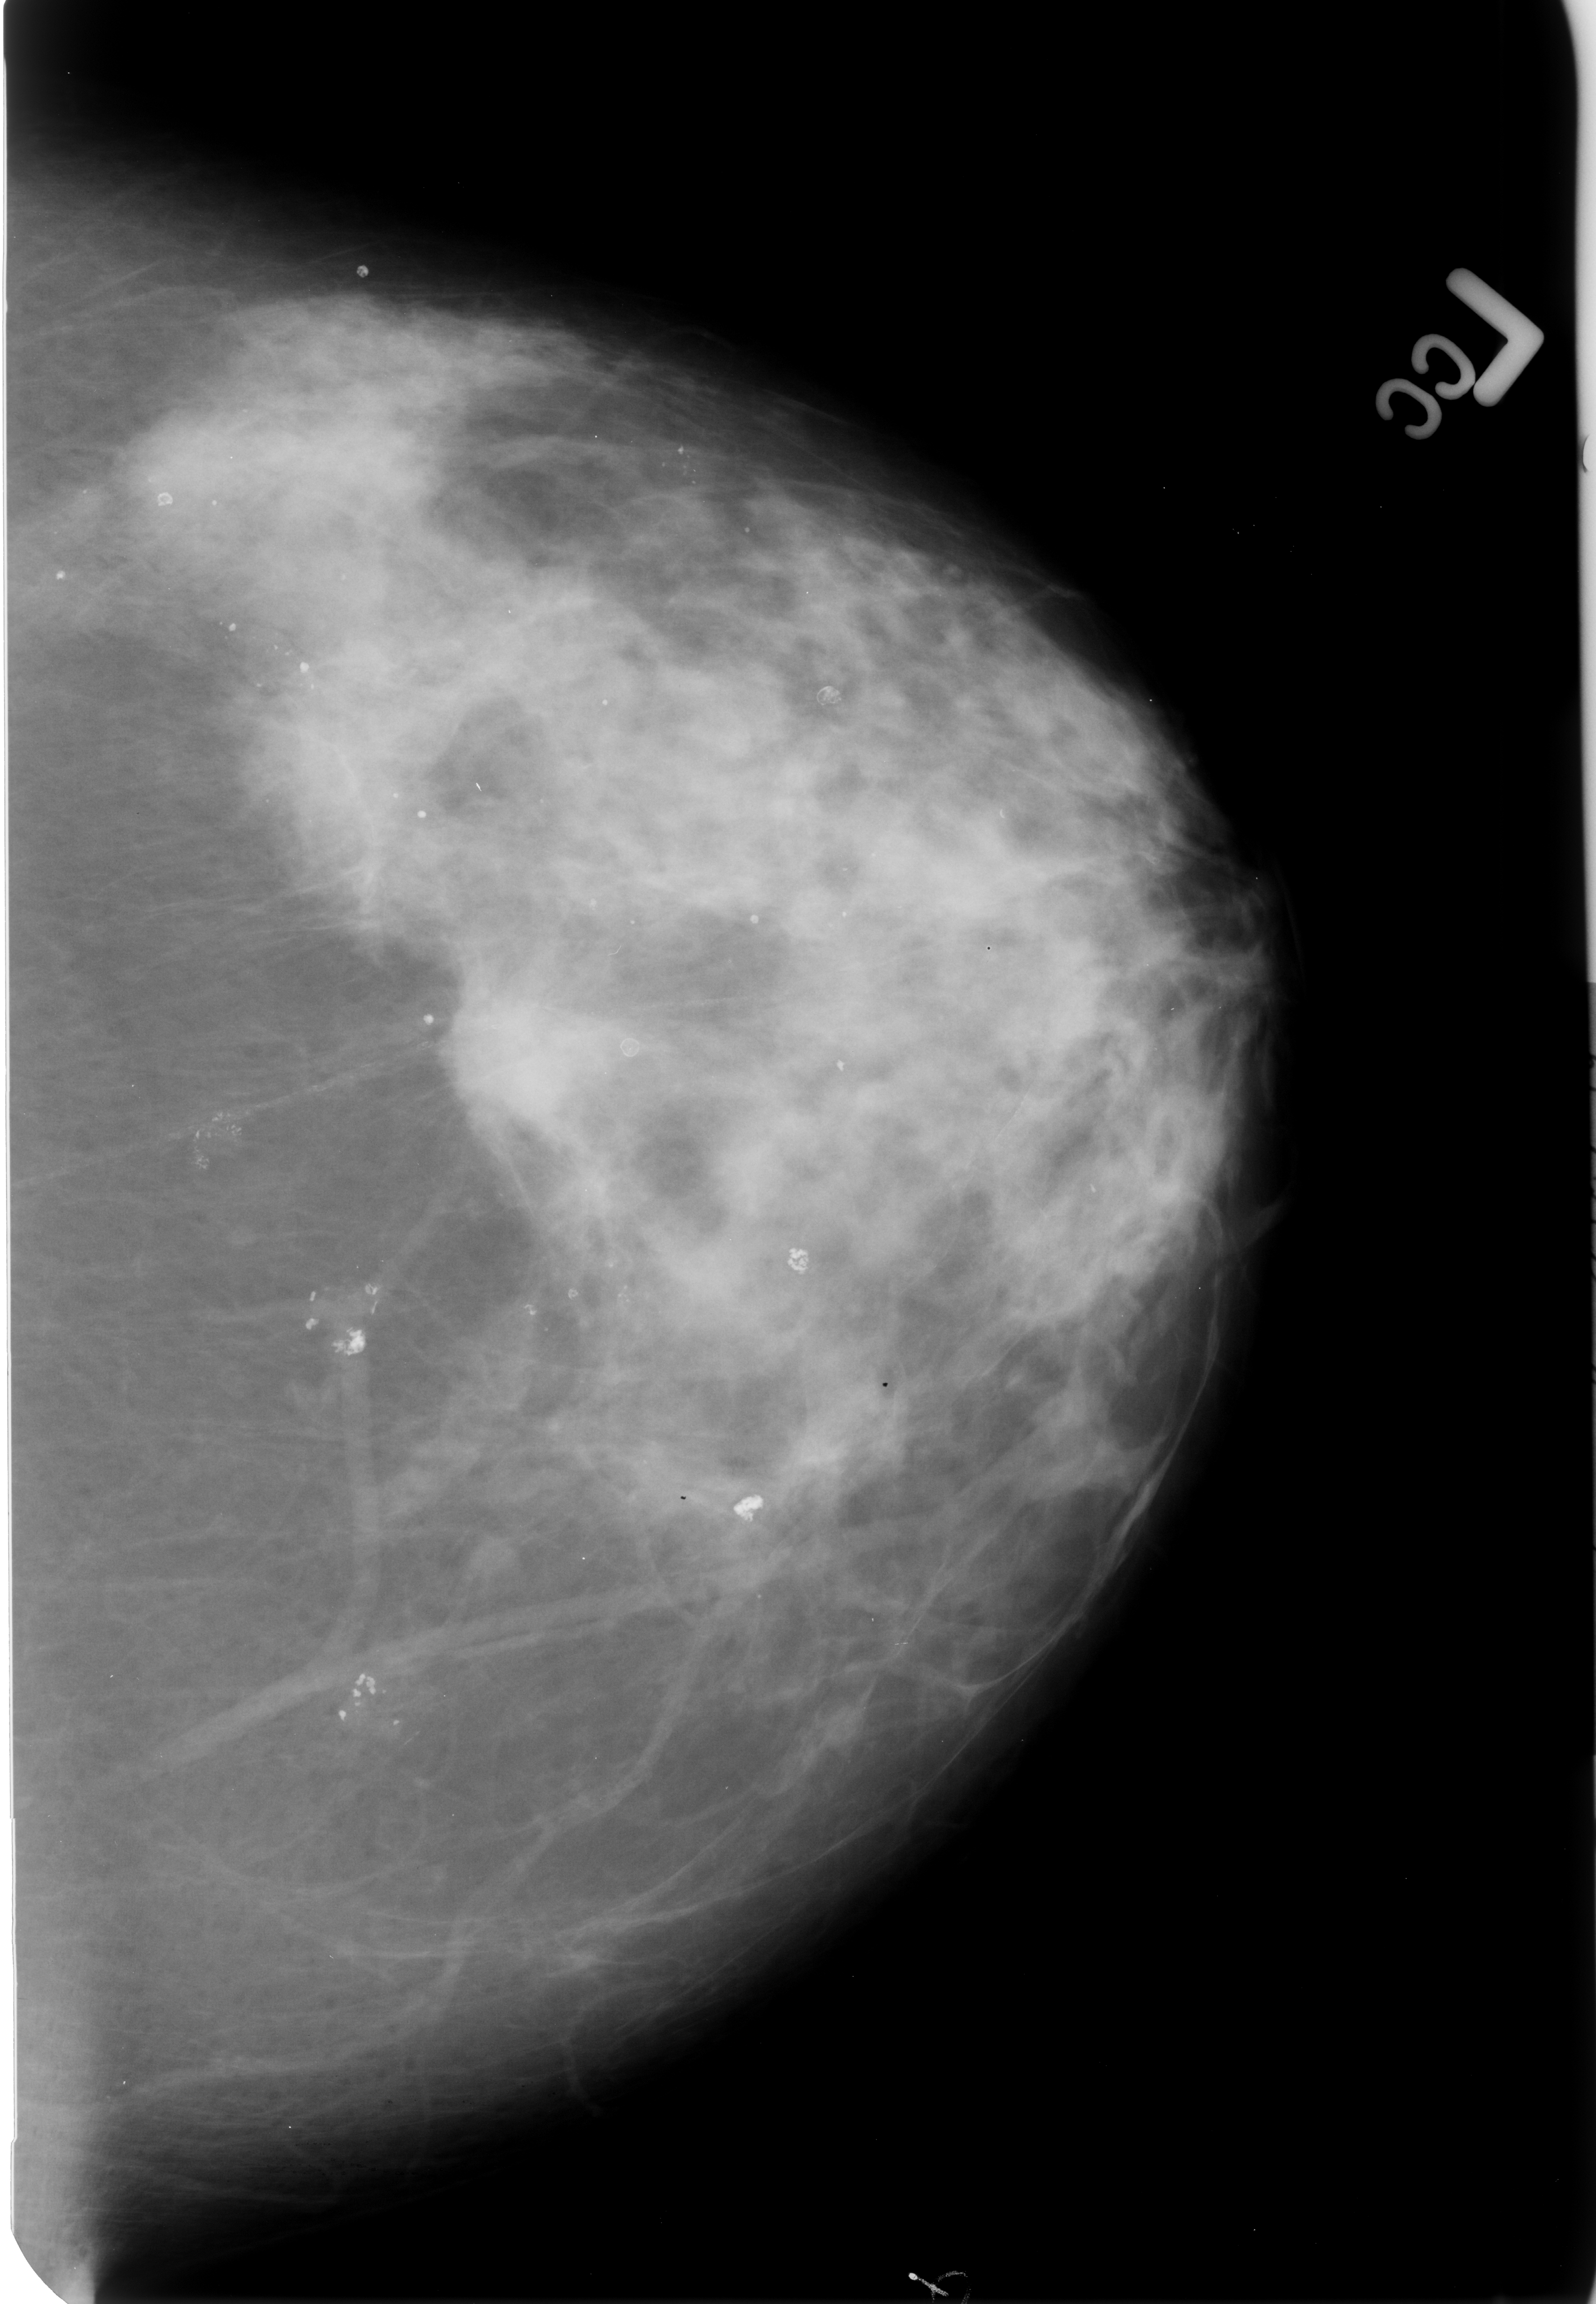
Mammogram (digitized film); left breast; craniocaudal (CC) view; breast composition: heterogeneously dense (BI-RADS density category 3 of 4).
Radiologist-marked abnormalities on this image: mass, shape irregular / architectural distortion, margins ill defined / spiculated; BI-RADS assessment category 4; subtlety rating 4 on a 1 (subtle) to 5 (obvious) scale; pathology result (as recorded, not read from the image): malignant.